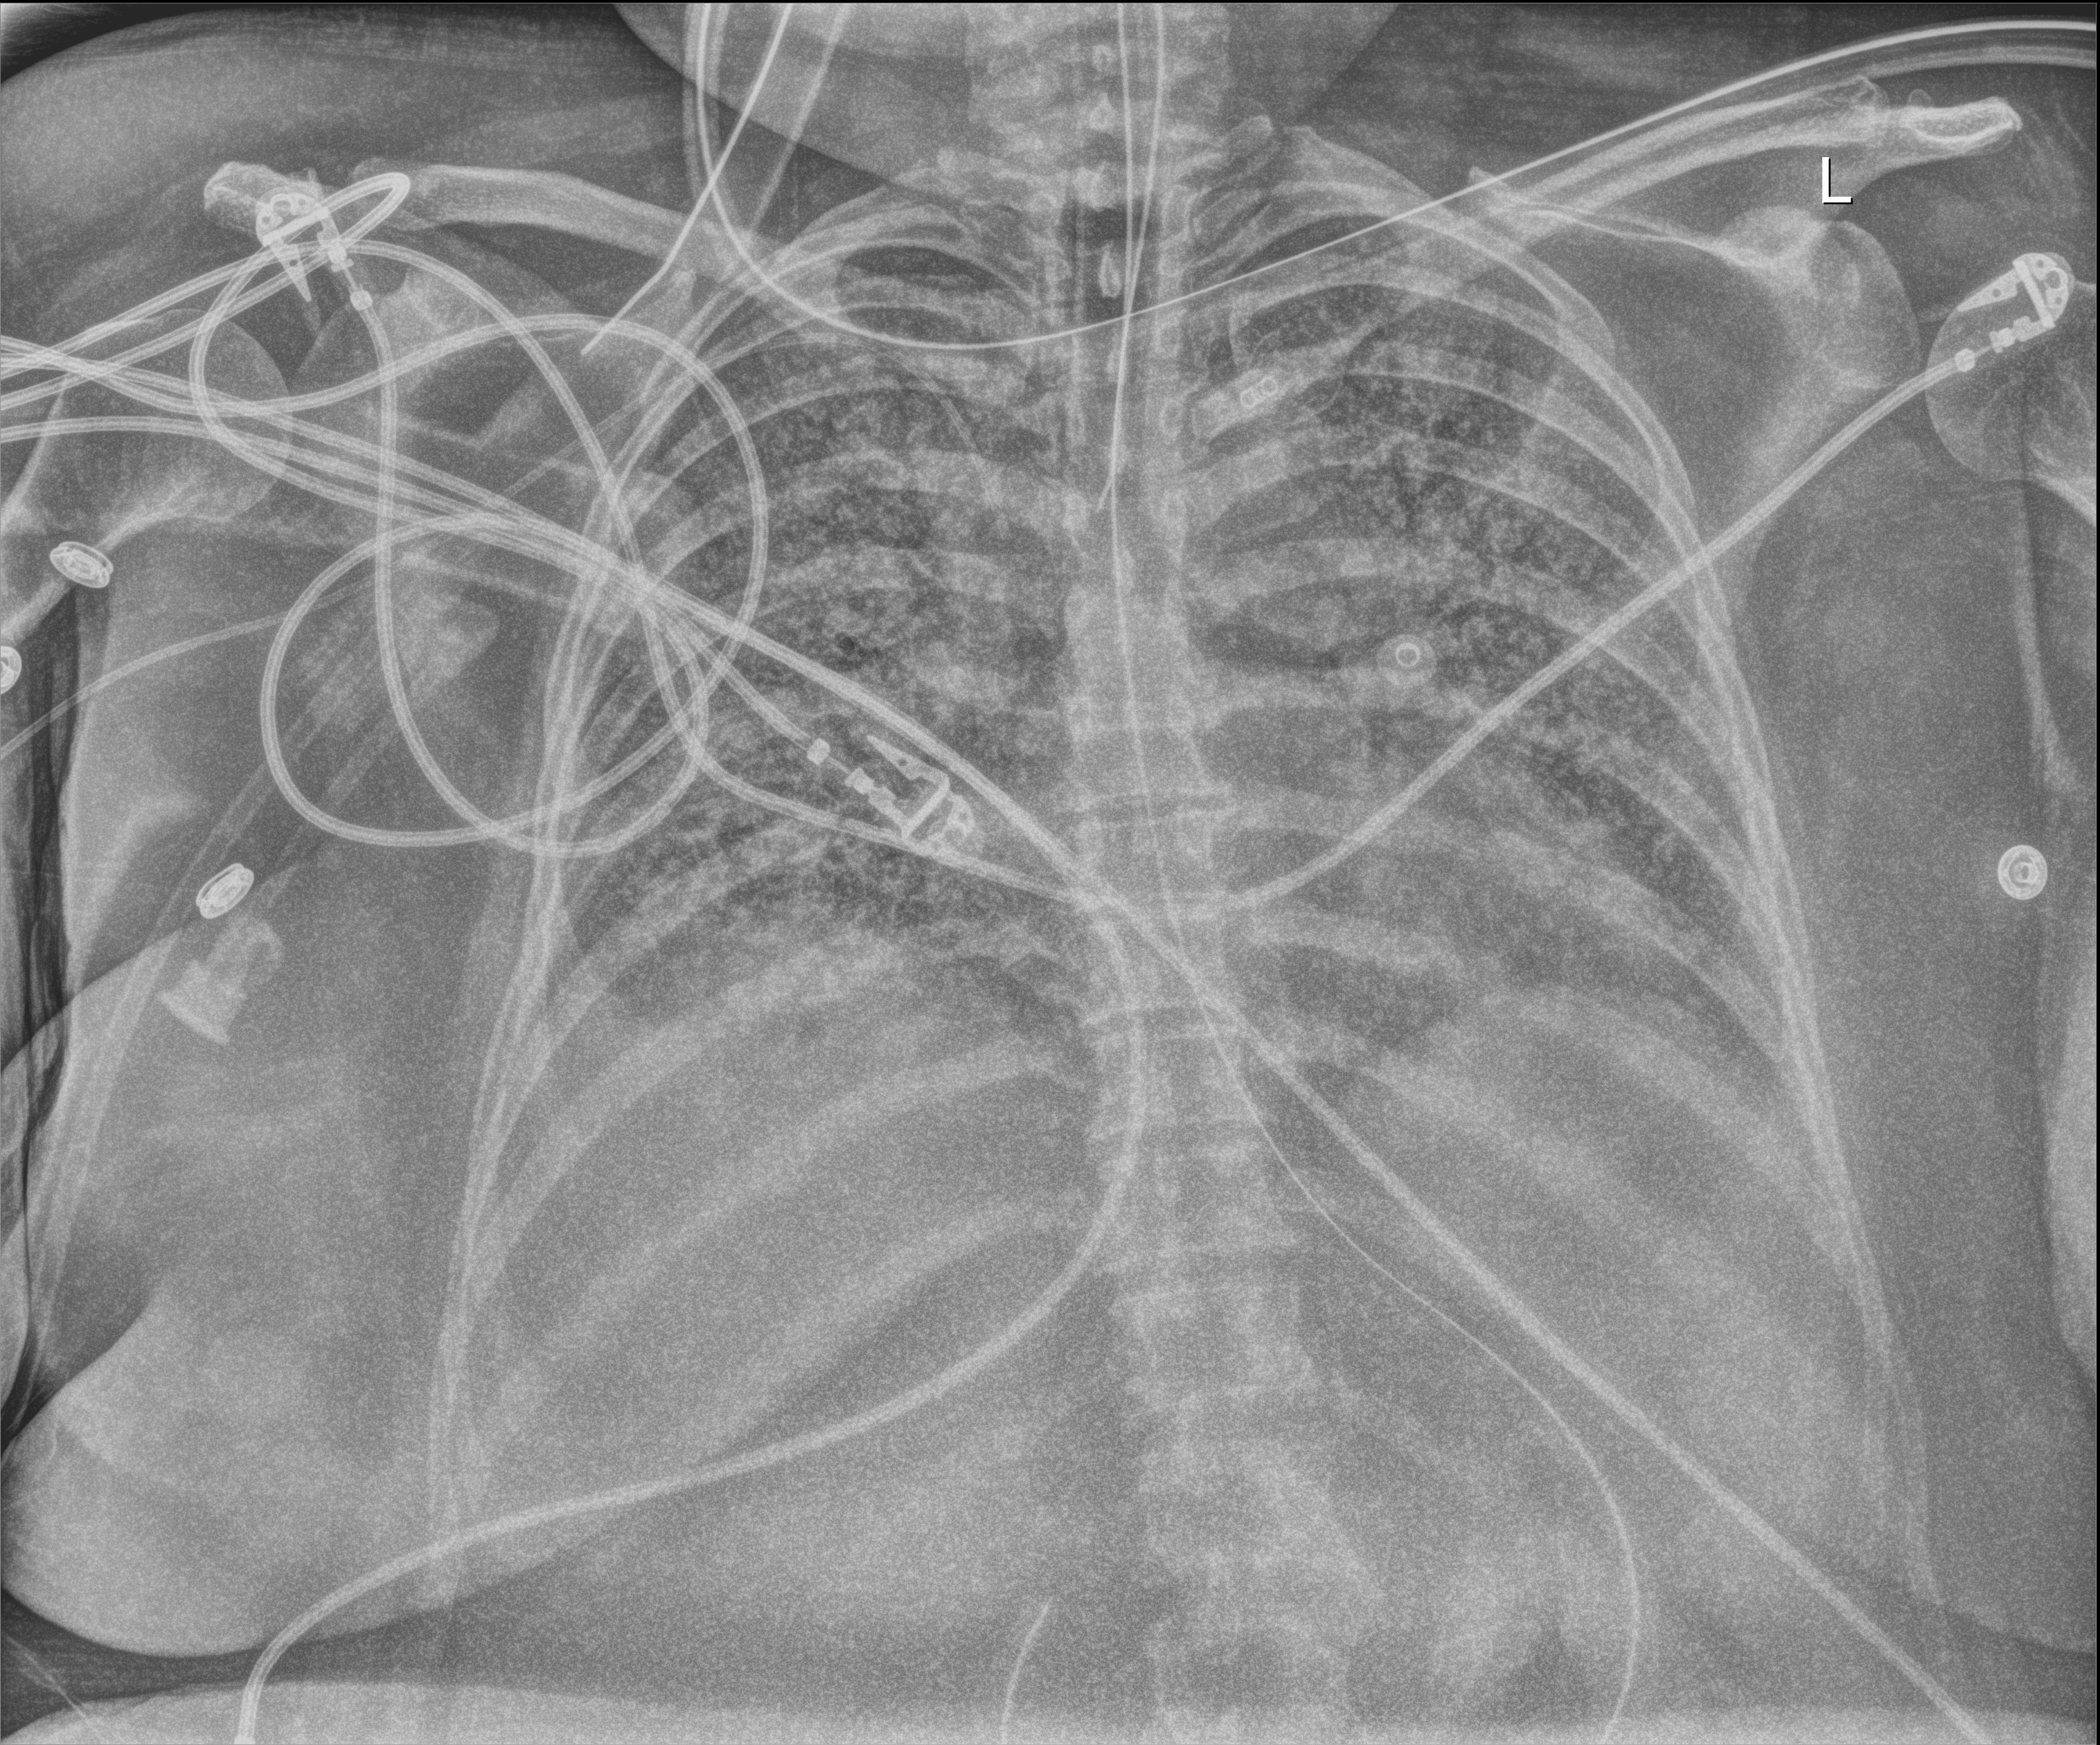
Portable chest radiograph; anteroposterior (AP) projection. Patient hospitalised with COVID-19; female, aged 18–59 years.
Admission-level facts for this patient (not findings on this image; timing relative to this image not recorded):
- mechanically ventilated during this hospital stay: yes
- chronic kidney disease (admission record): no
- admitted to intensive care during this hospital stay: yes